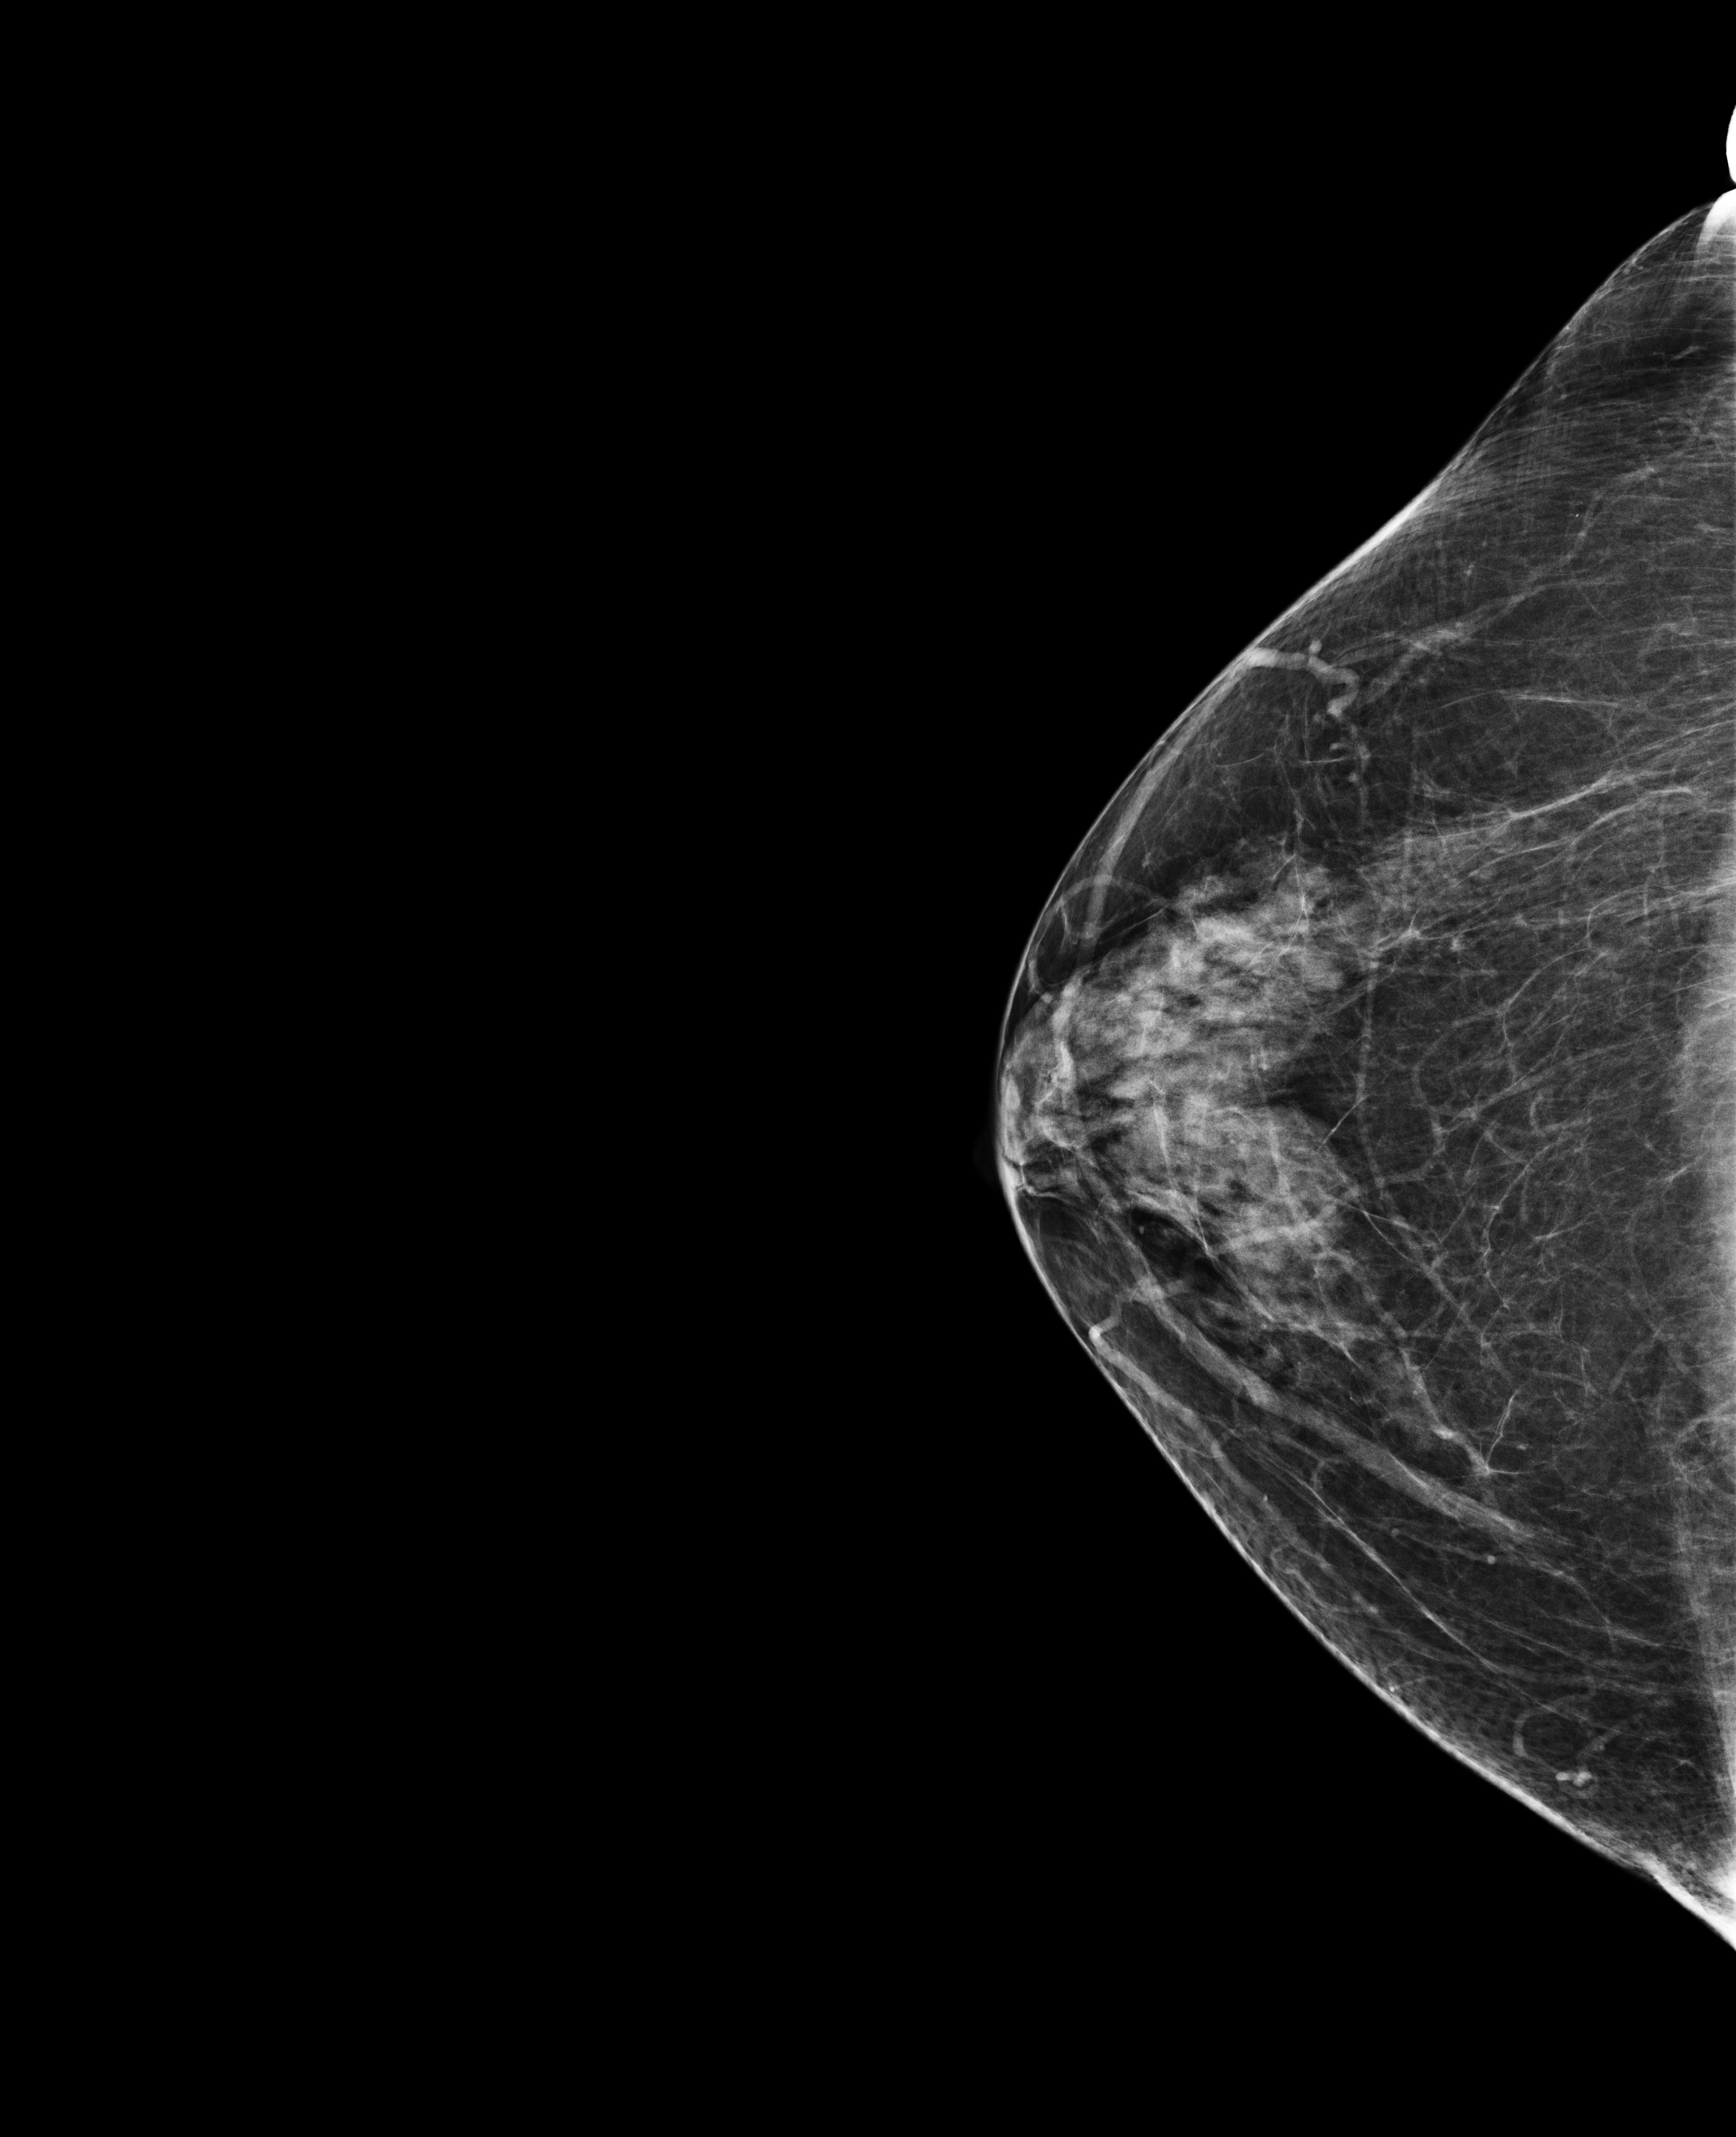
Annual screening mammography examination.
Image type: full-field digital mammogram. Breast: right. Projection: CC view.